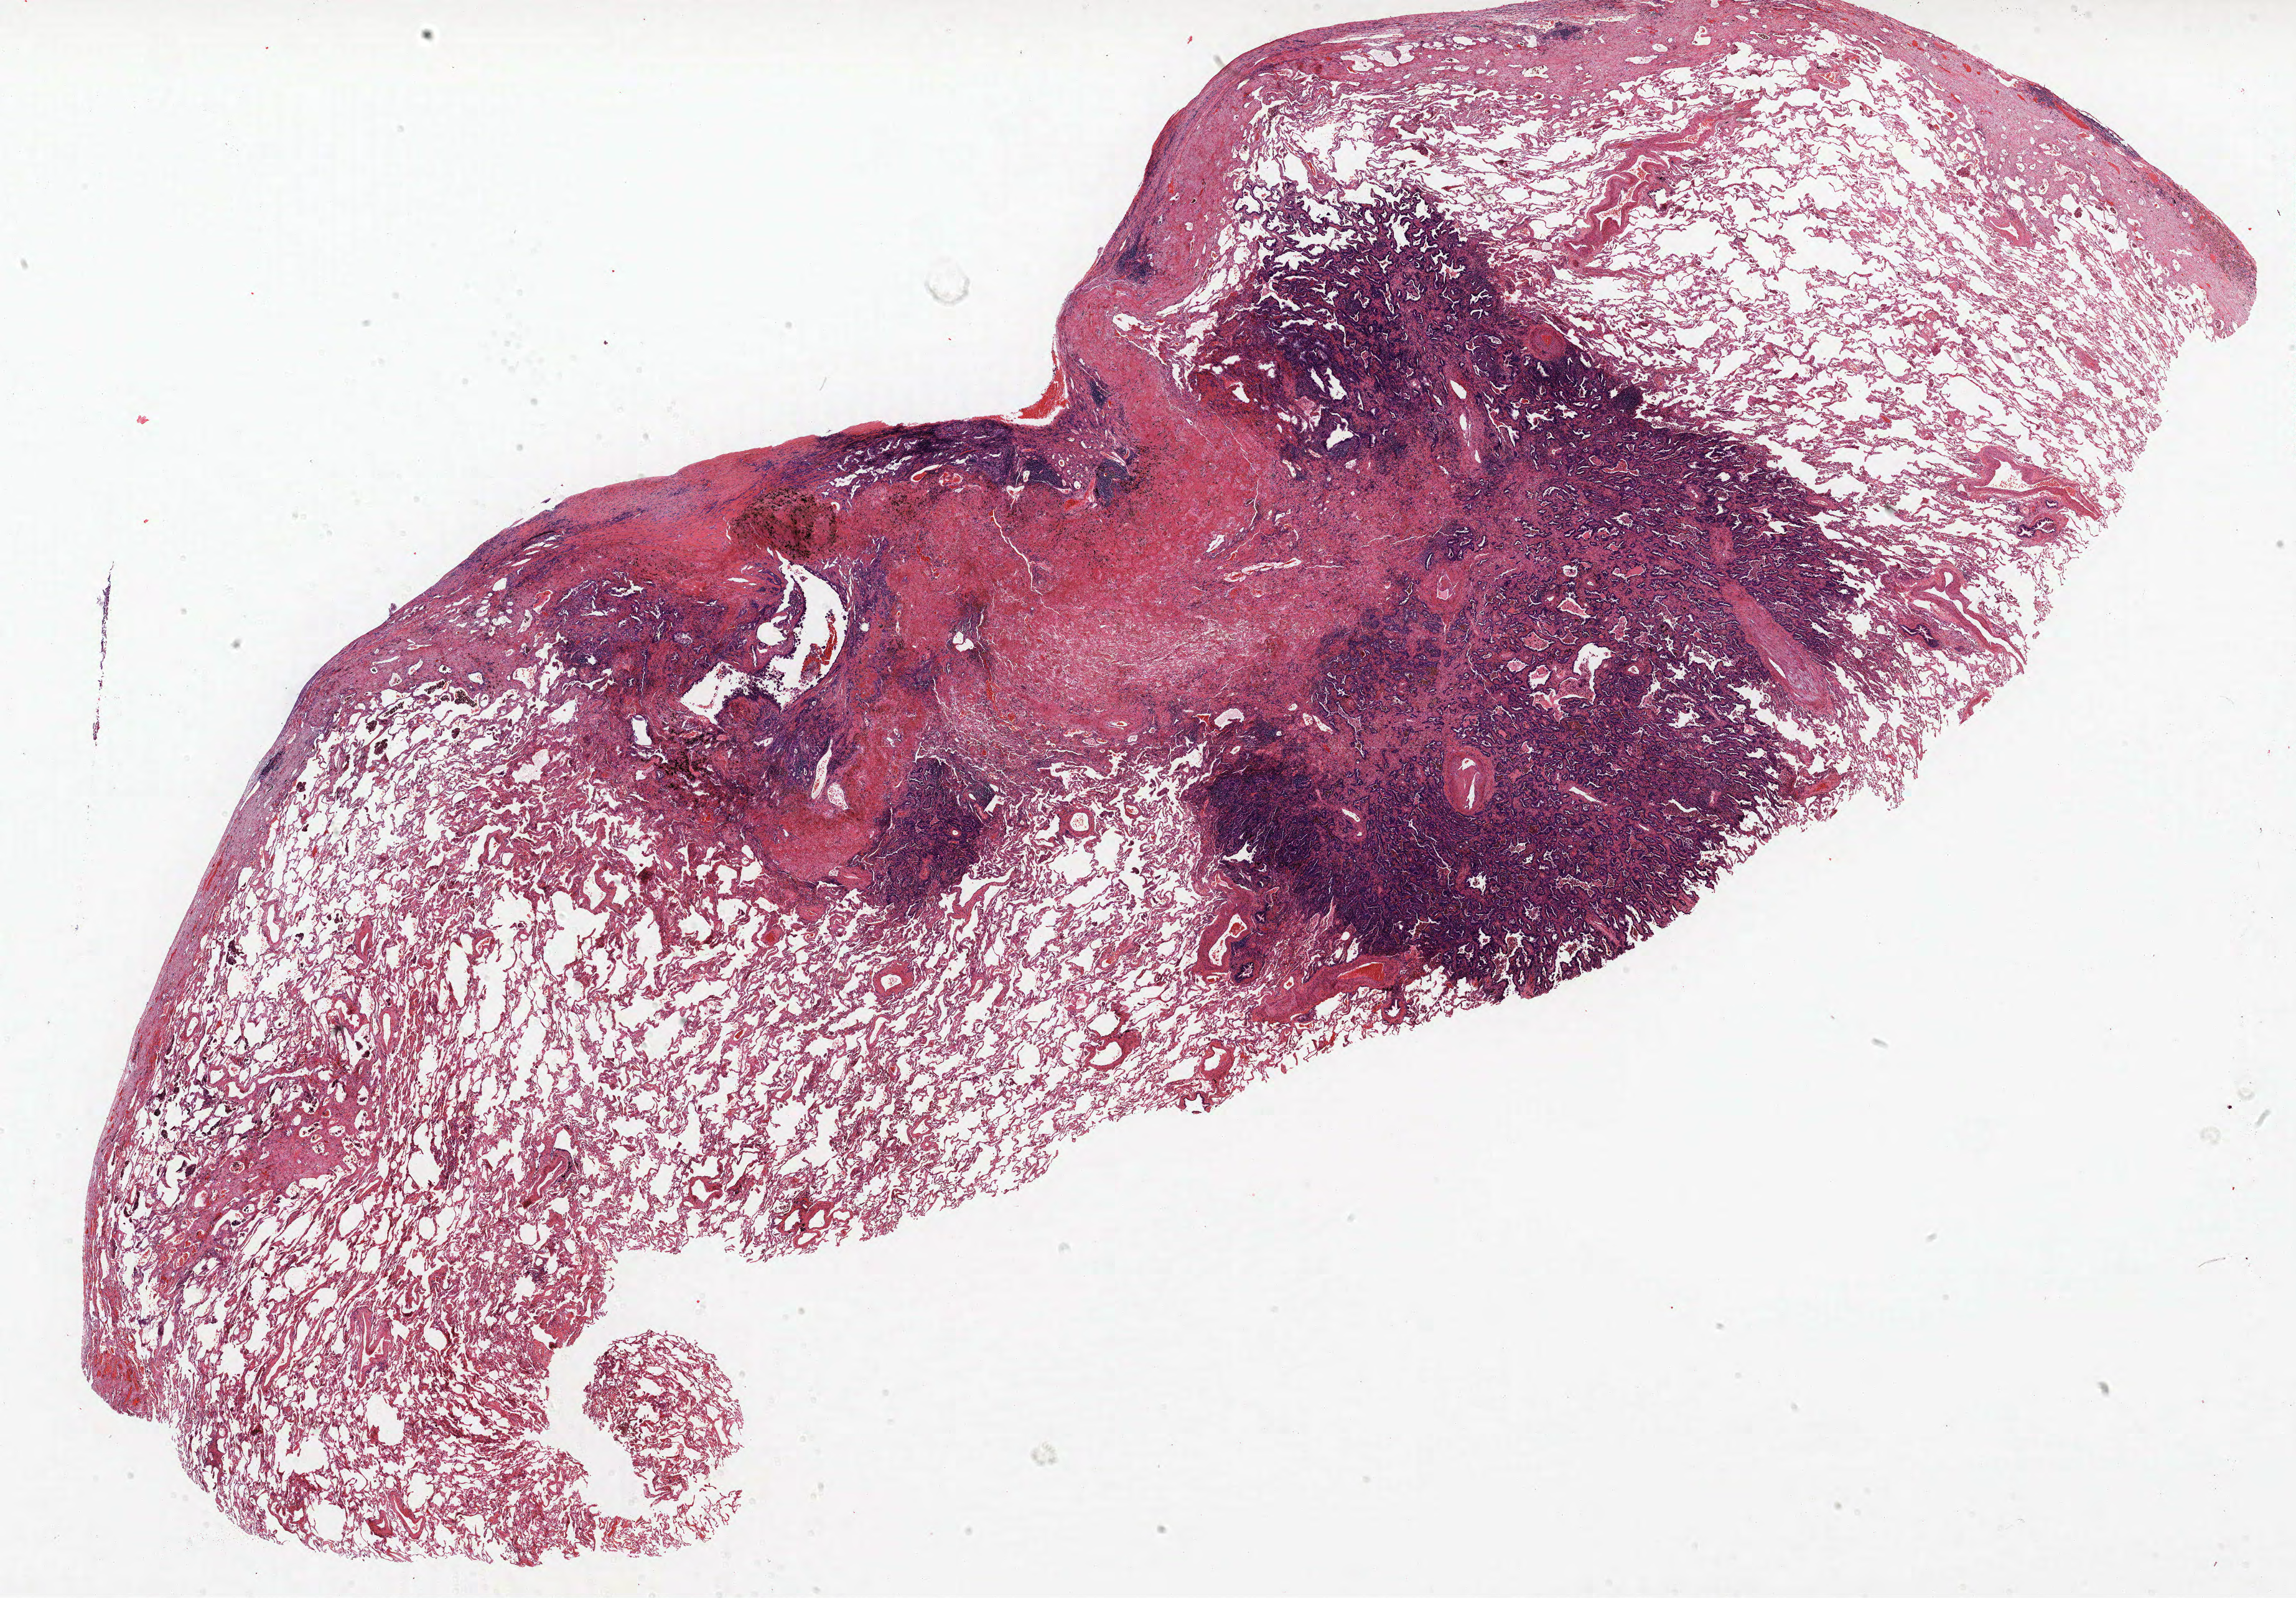
Whole-slide histology image, H&E-stained, low-resolution overview of the scanned area, about 29.5 x 20.5 mm (slide scanned at 40x), formalin-fixed paraffin-embedded (FFPE) section, lung. Male patient, aged 62 at enrolment. Grade: well differentiated (G1).
Stage (AJCC 6th edition): IB. Participant's lung-cancer diagnosis: Adenocarcinoma, NOS (ICD-O-3 8140/3). Primary tumour location (clinical record): left upper lobe. Tumour size (pathology): 17 mm.